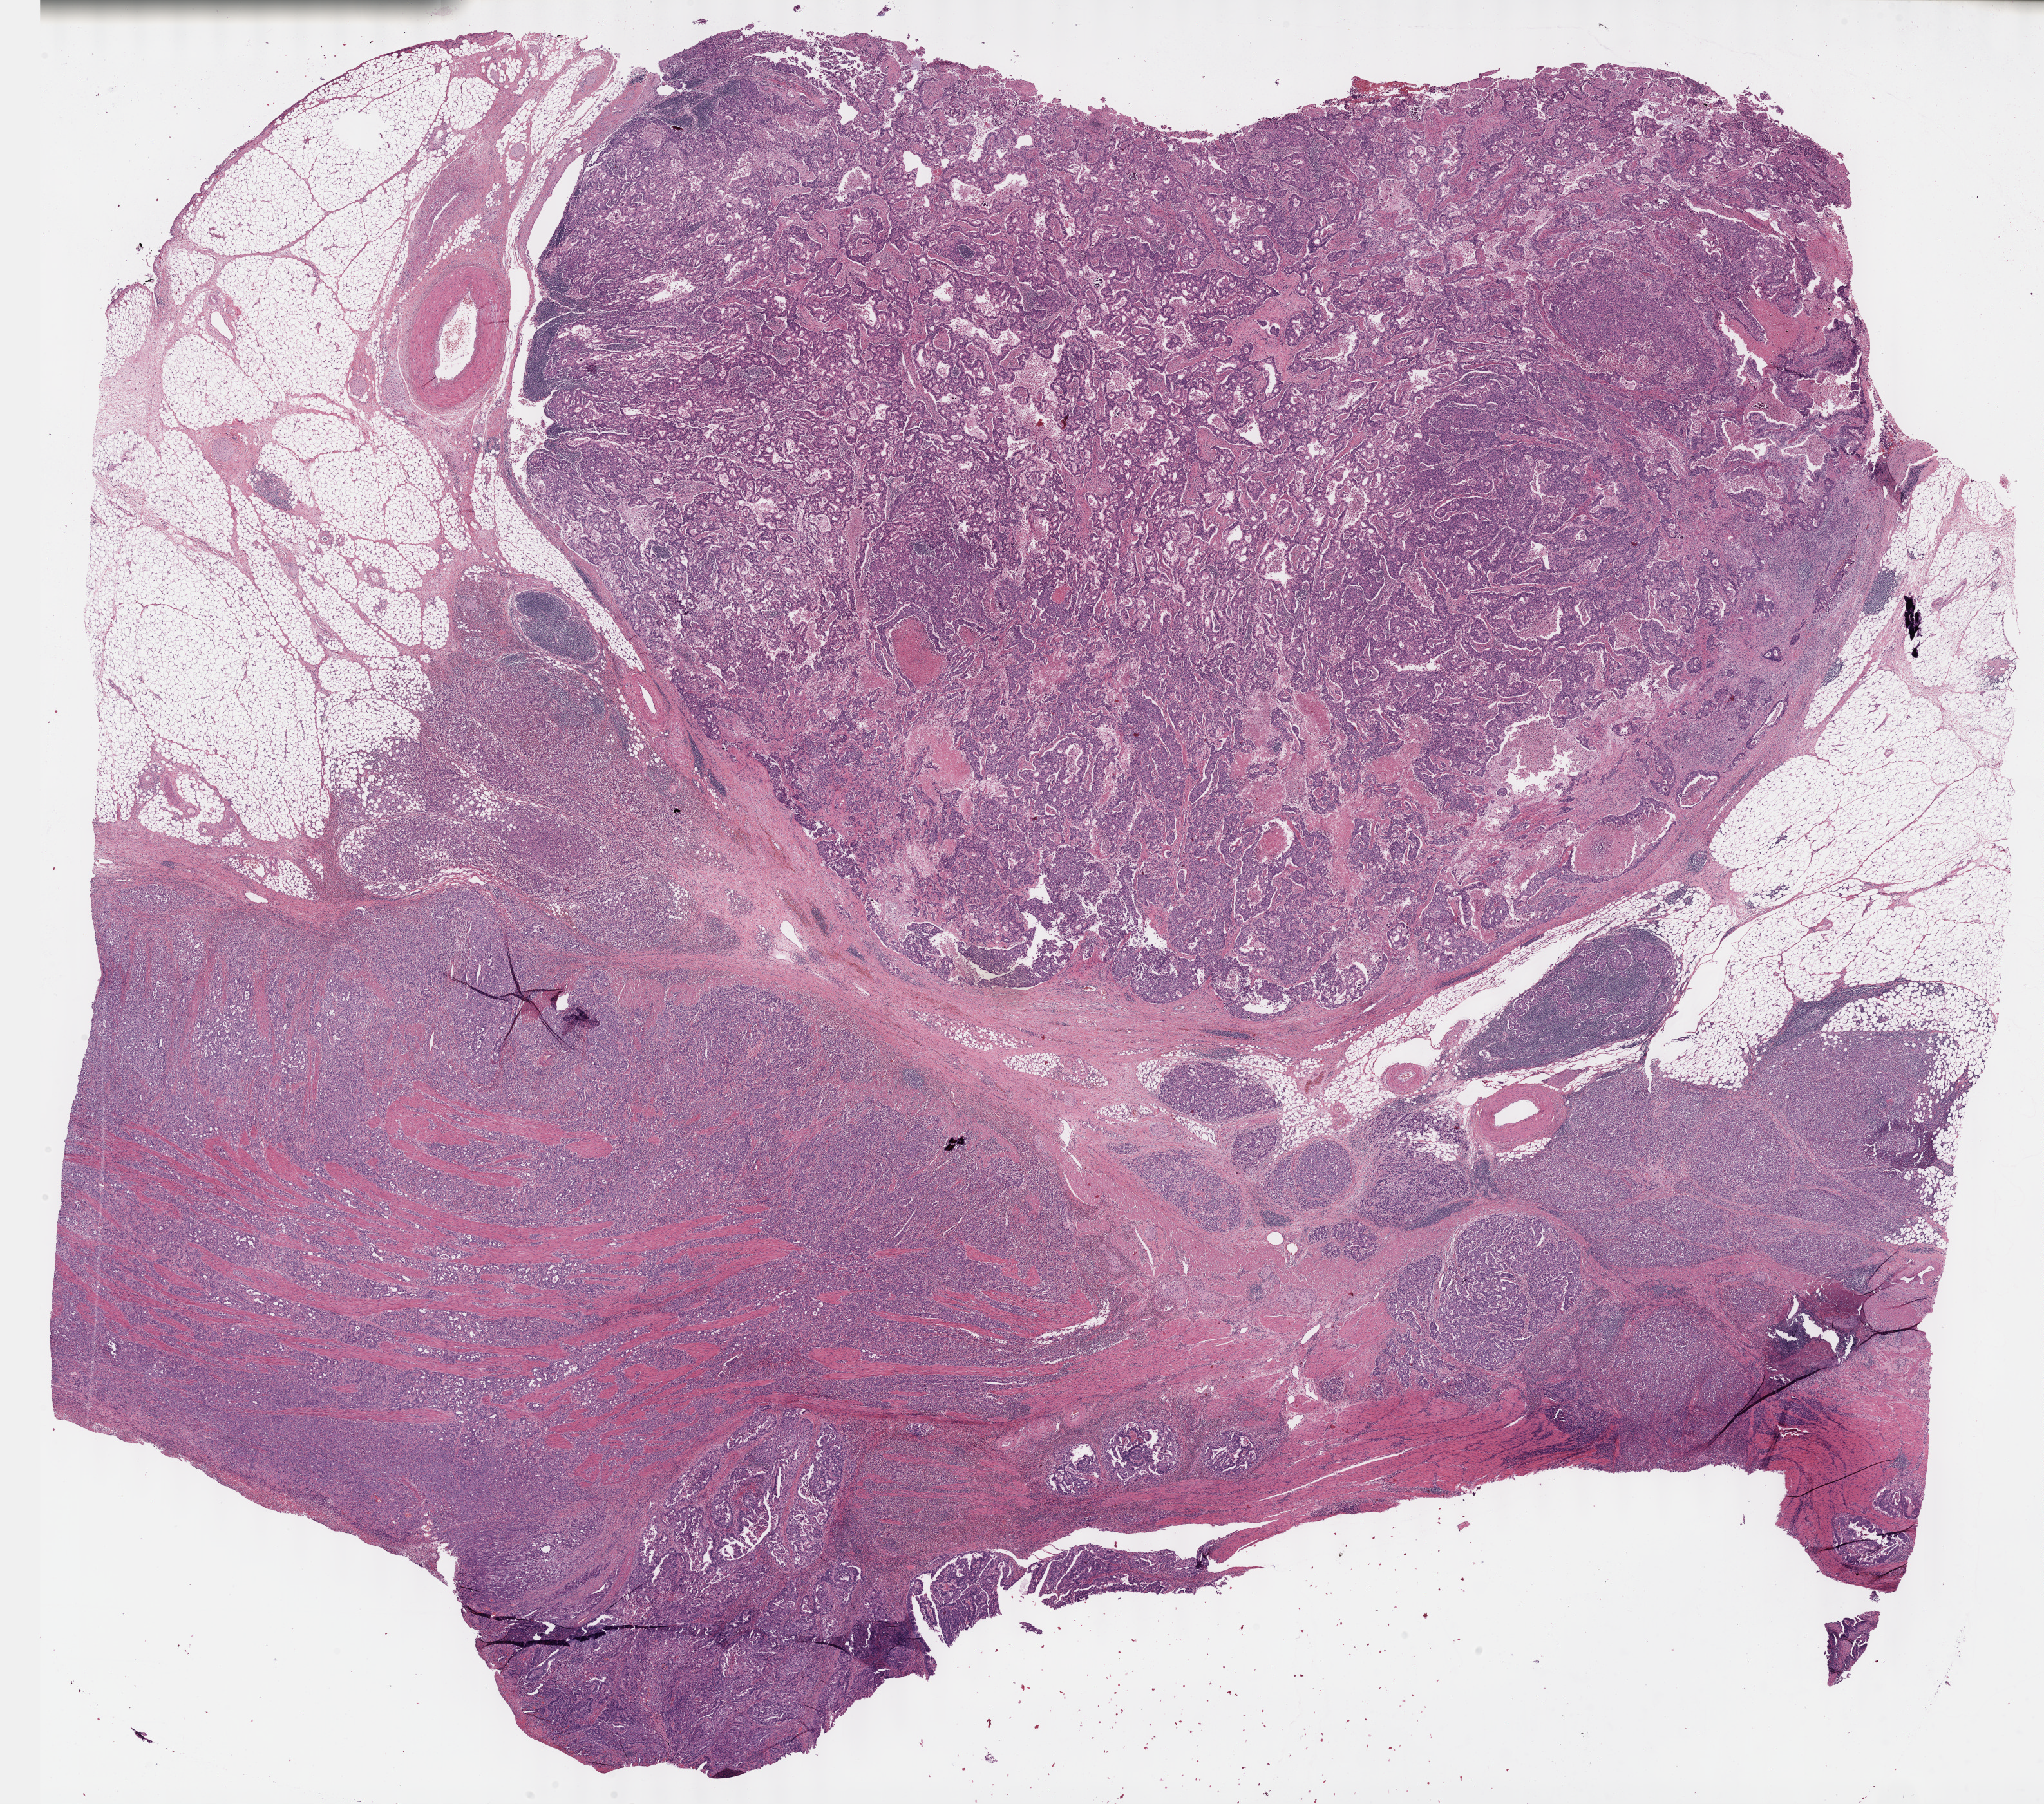
Hematoxylin and eosin (H&E) stained whole-slide image, a low-resolution overview of the entire scanned area, about 25.7 x 22.6 mm. Formalin-fixed paraffin-embedded (FFPE) diagnostic section. Sample: primary tumour, stomach. Patient: male, age at initial diagnosis 63 years. Histologic grade: GX (grade cannot be assessed).
TNM: T4b N1 M0. AJCC pathologic stage: IIIB (7th edition). Lymph nodes positive (case pathology): 2 of 32 examined. Diagnosis: Tubular adenocarcinoma (body of stomach).